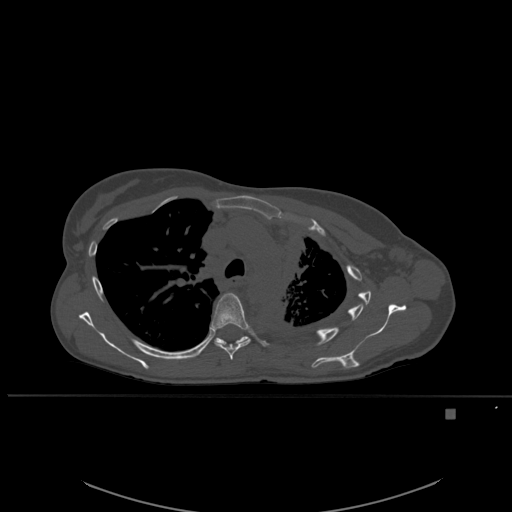
CT including the spine, one axial slice. Position 395 of 537 along the scan axis. Bone window (W 1800 / L 400 HU). 1.5 mm slice thickness. 512 × 512 image matrix. Female patient, age 45 years. From the clinical record (not read from this slice): primary cancer: lung.
Structures marked on this image (semi-automatic segmentation, software-assisted and operator-edited):
- T4 vertebra: bounding box <218,343,222,345> (left, top, right, bottom; pixels)
- T5 vertebra: <210,293,251,360>
- T6 vertebra: <214,336,249,345>